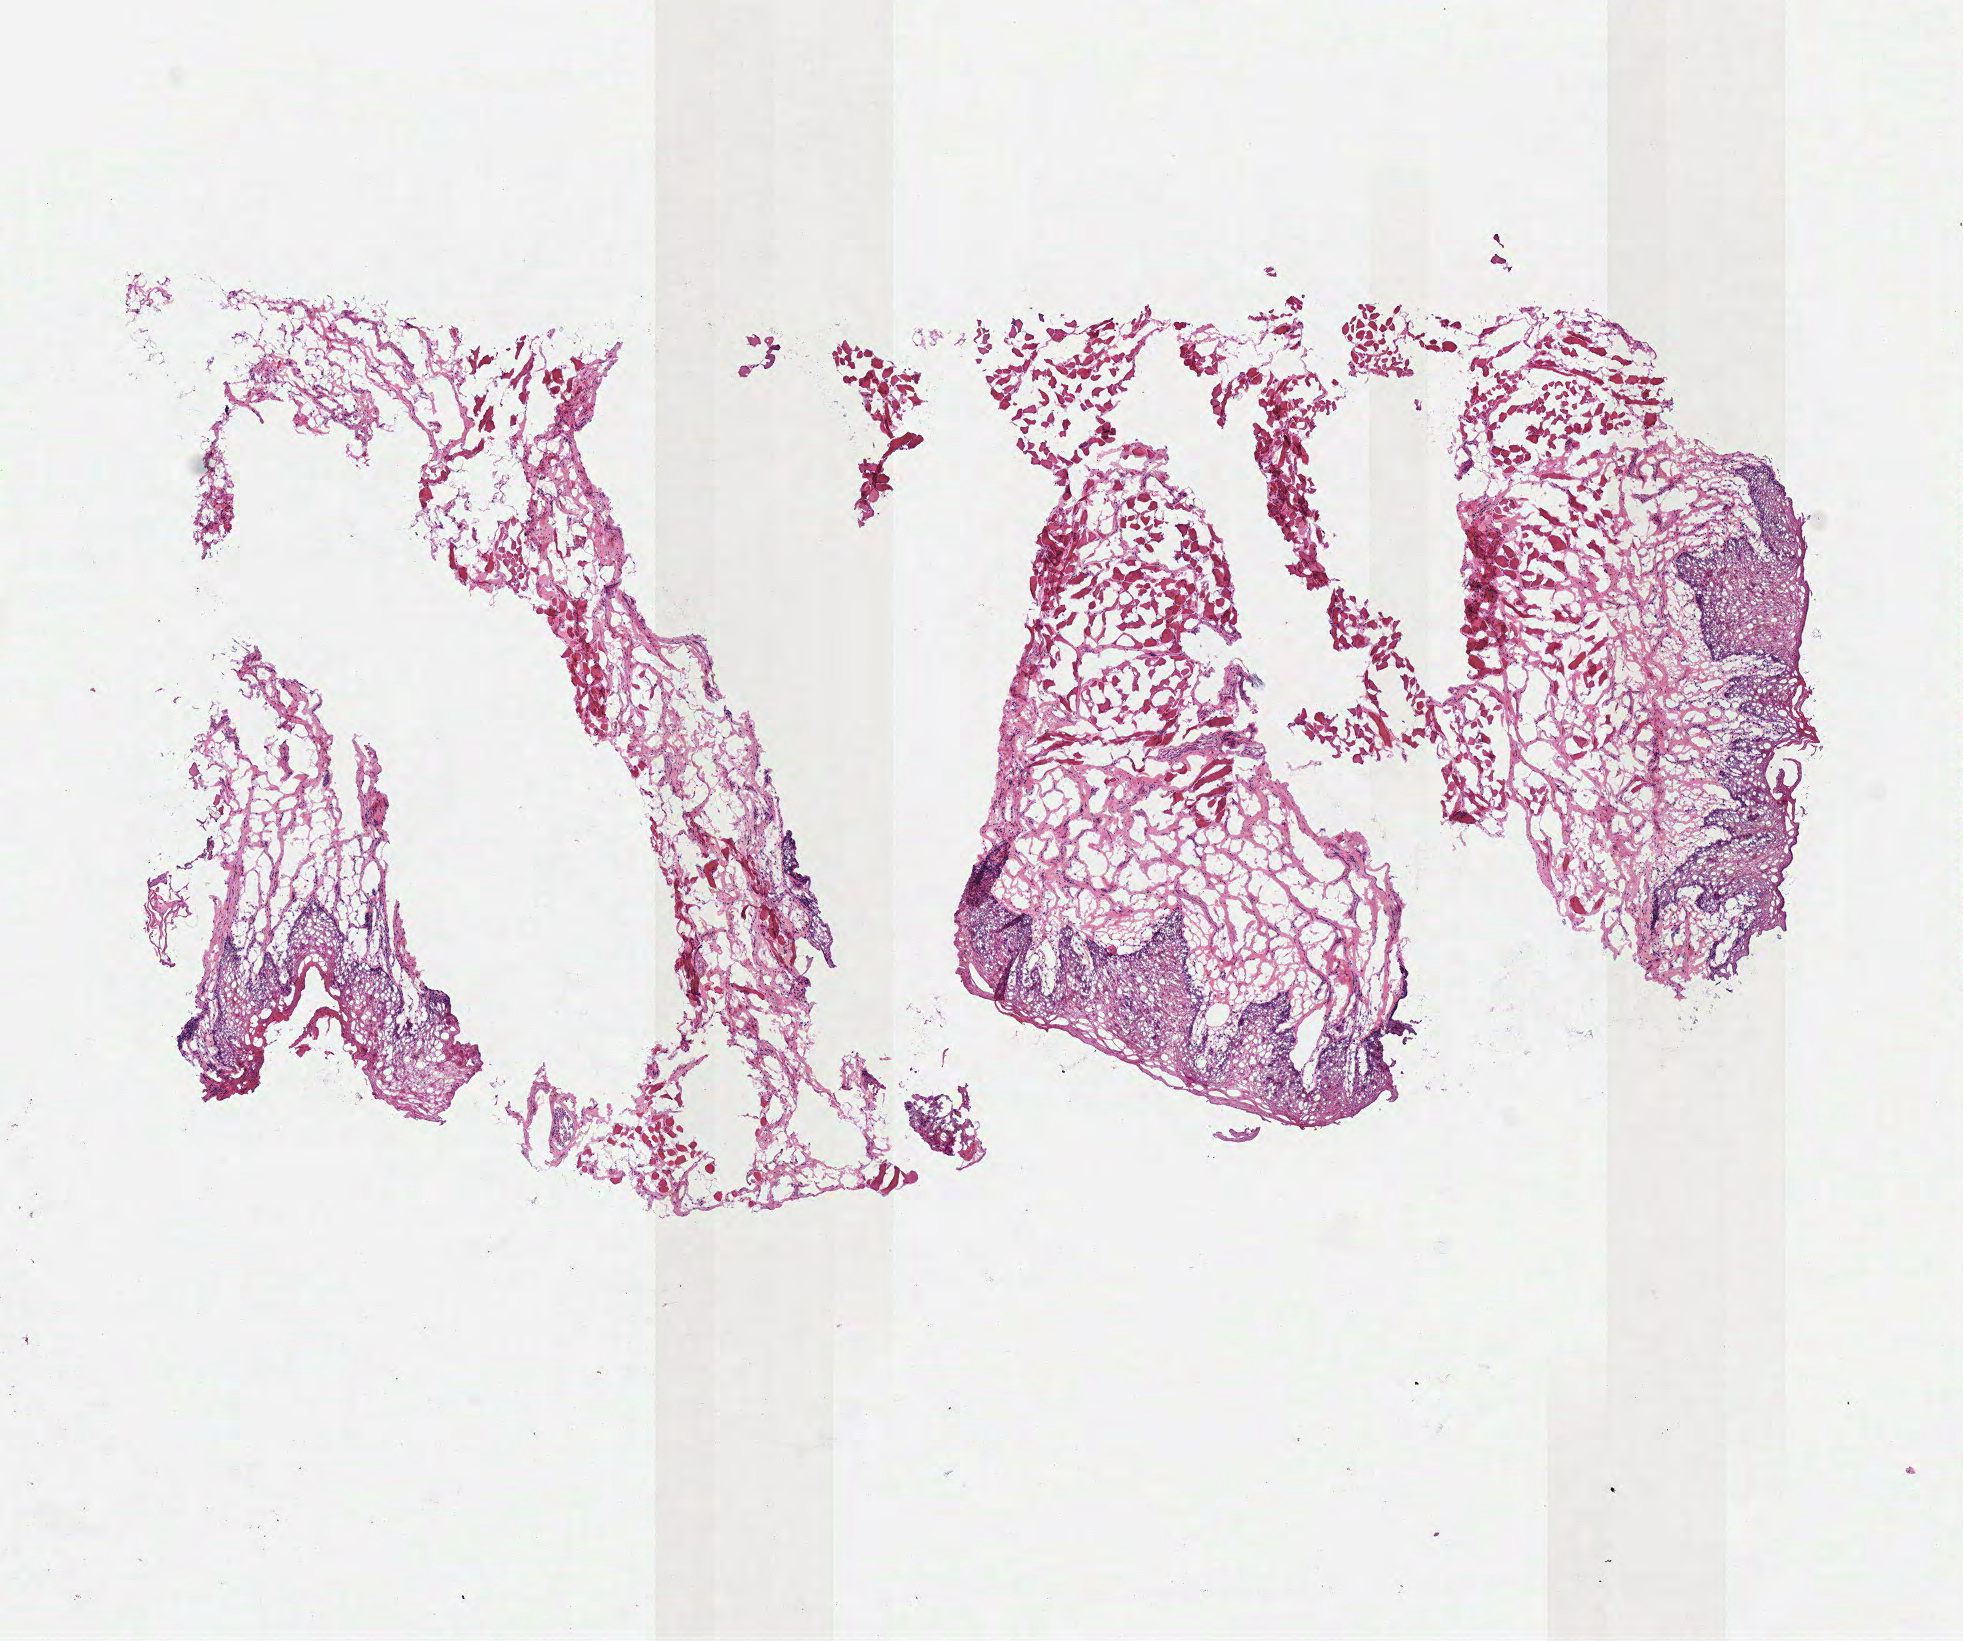
H&E whole-slide image, a low-resolution overview of the entire scanned area, about 7.7 x 6.5 mm. Frozen section from the top of the tissue portion. Solid tissue normal (non-tumour tissue) sample from the head and neck. Male, age 57 years at initial diagnosis.
• this section: solid tissue normal sample (biorepository sample class)
• patient diagnosis: Squamous cell carcinoma, NOS (tongue, NOS)